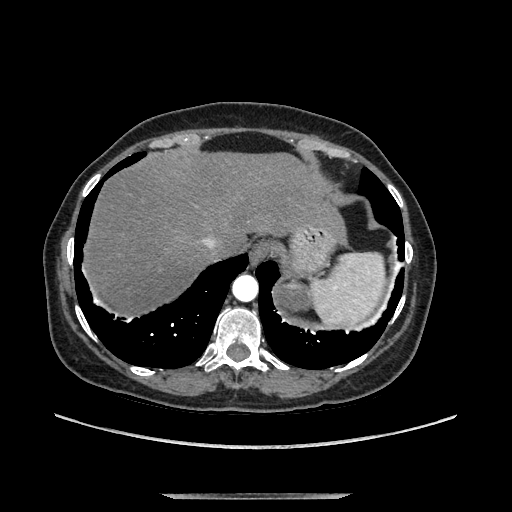
Contrast-enhanced abdominal CT, one axial slice. Position 119 of 169 along the scan axis. Soft-tissue window (W 400 / L 40 HU). 512 × 512 image matrix, field of view 400 × 400 mm. Female patient. Case-level facts recorded for this patient, not image findings: diagnosis: adrenocortical carcinoma; tumour side: left adrenal; tumour size at pathology: 9 cm.
Annotated regions visible in this slice (semi-automatically segmented with operator editing):
- mass: bounding box <275,284,309,311> (left, top, right, bottom; pixels)